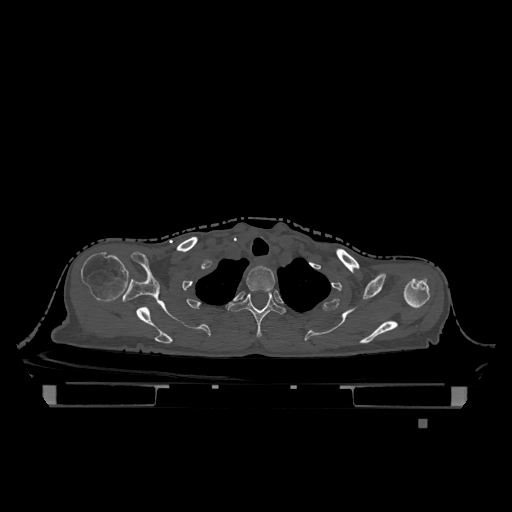
CT including the spine, one axial slice. Slice 973 of 1317 in the series (ordered by position). Bone window (W 1800 / L 400 HU). 512 × 512 image matrix, field of view 500 × 500 mm. Patient: female, 74 years. Case-level facts recorded for this patient, not image findings: primary cancer: lung.
Structures marked on this image (semi-automatic segmentation, software-assisted and operator-edited):
- T1 vertebra: bounding box (x1, y1, x2, y2) in pixels: (246, 265, 275, 292)
- T2 vertebra: (228, 291, 286, 338)